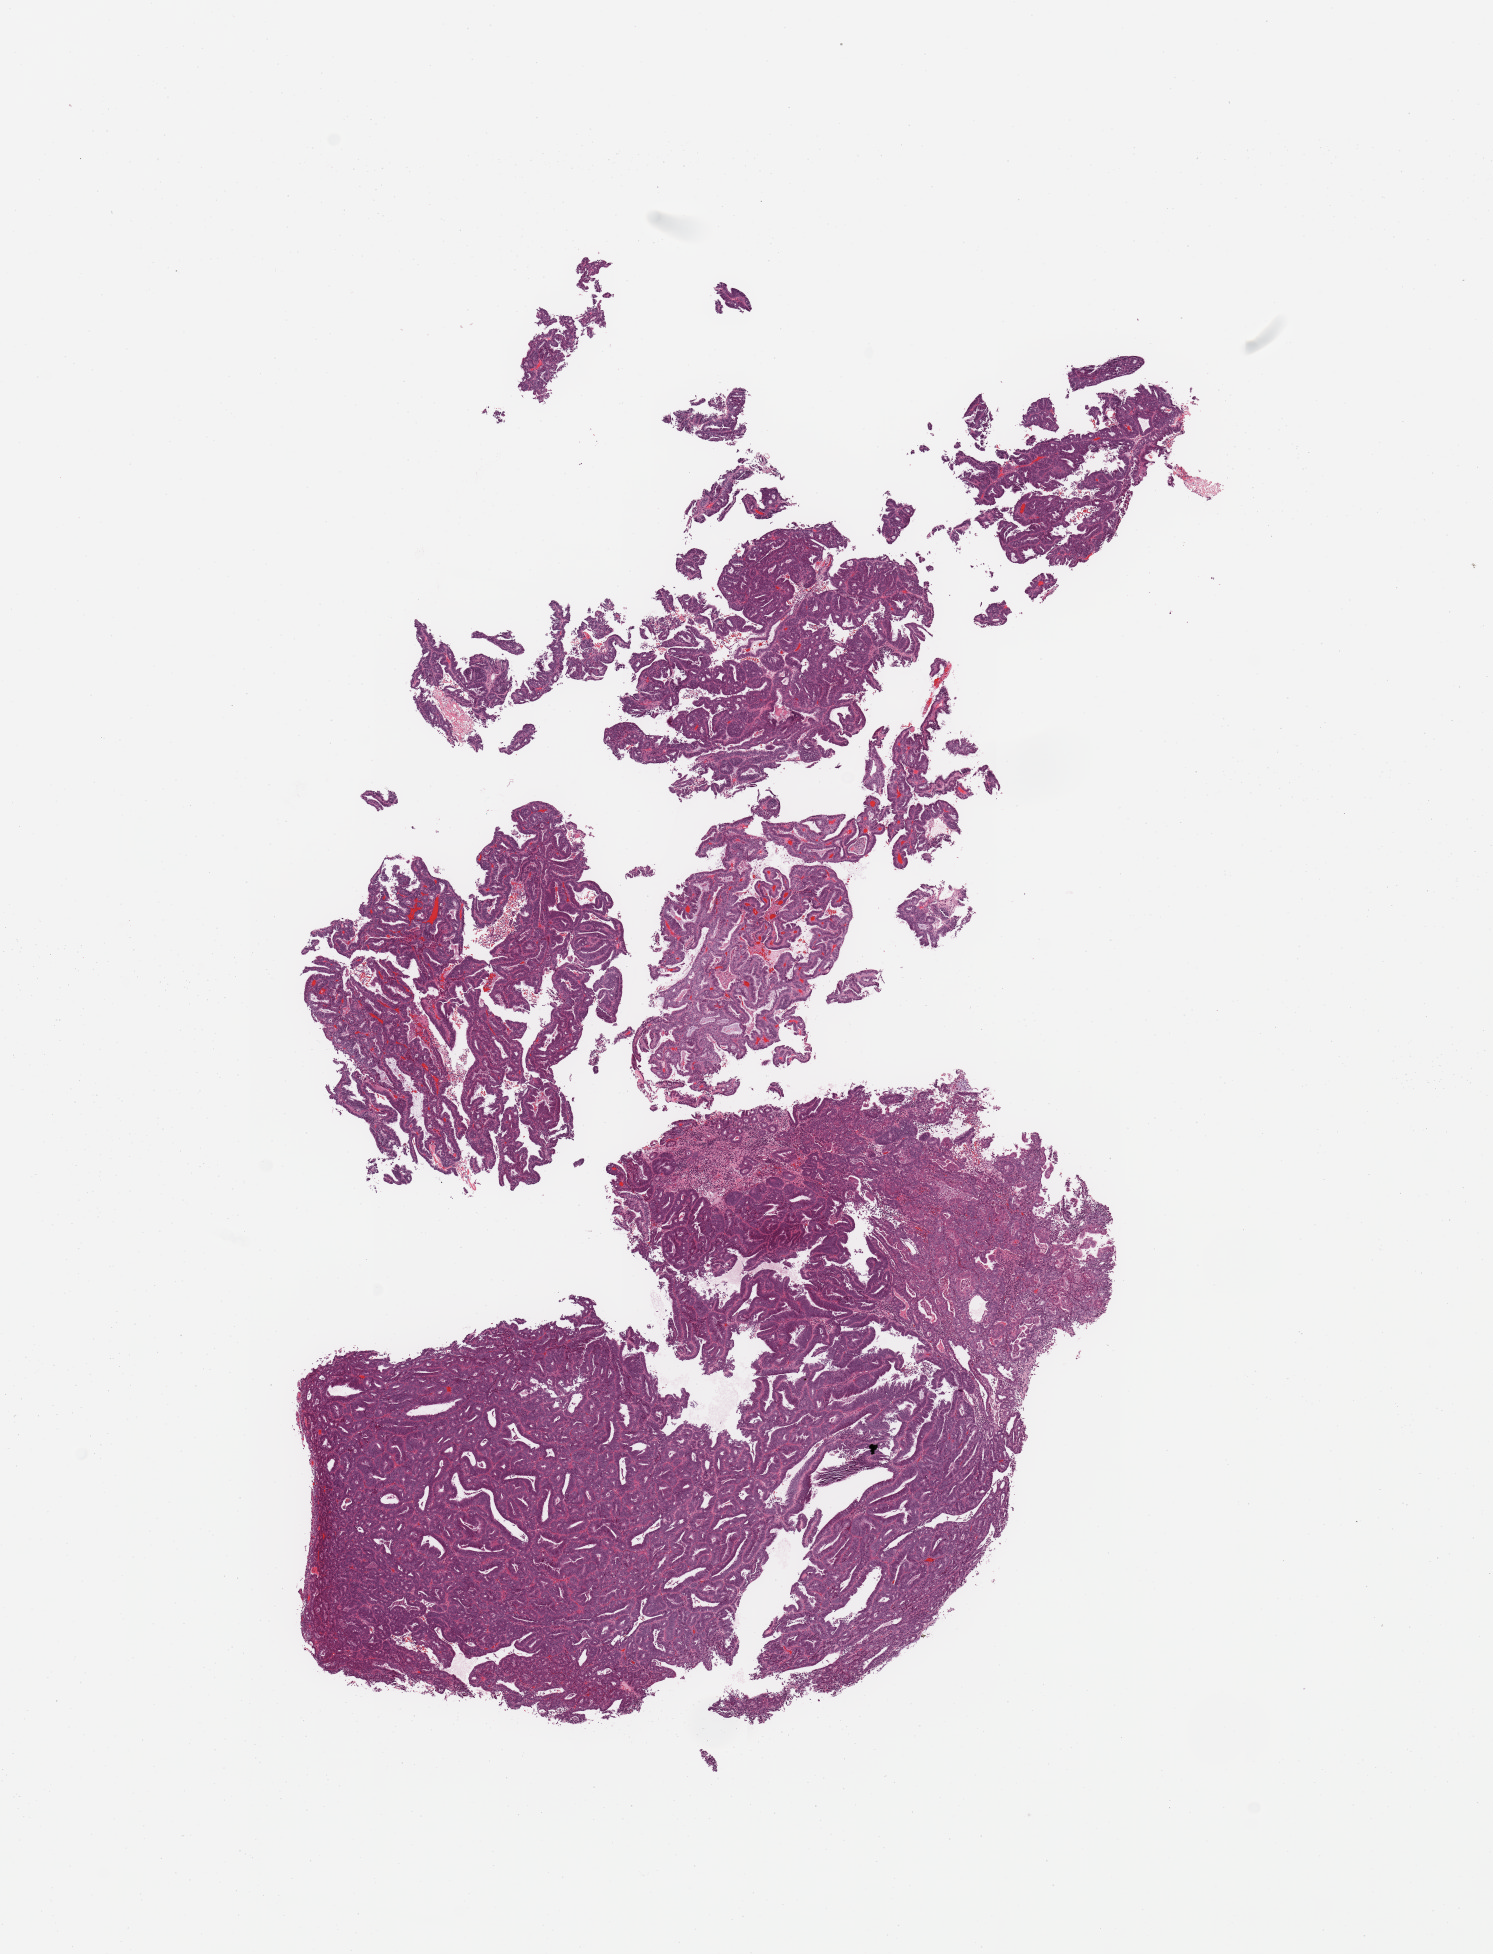
Whole-slide histology image, H&E-stained, low-resolution overview of the scanned area, about 11.8 x 15.5 mm (acquisition: 20x scan). Tumour tissue sample, uterus. 75-year-old female patient. Histologic grade: G2 (moderately differentiated).
• AJCC pathologic stage: I
• primary tumour site (as recorded): anterior endometrium
• diagnosis: Endometrioid adenocarcinoma, NOS